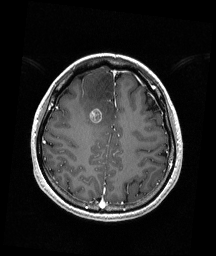
Brain MRI from a brain-tumour surgery series, one axial slice; slice 58 of 192 in the series (ordered by position); T1-weighted post-contrast; 1 mm slice thickness; 216 × 256 image matrix. Case-level facts recorded for this patient, not image findings: histopathology: Astrocytoma; WHO grade: 4; IDH mutation: yes; tumour location: Right Frontal.
Outlined on this slice (outlined manually by an expert reader):
- tumour: box from (x=90, y=108) to (x=102, y=123) px